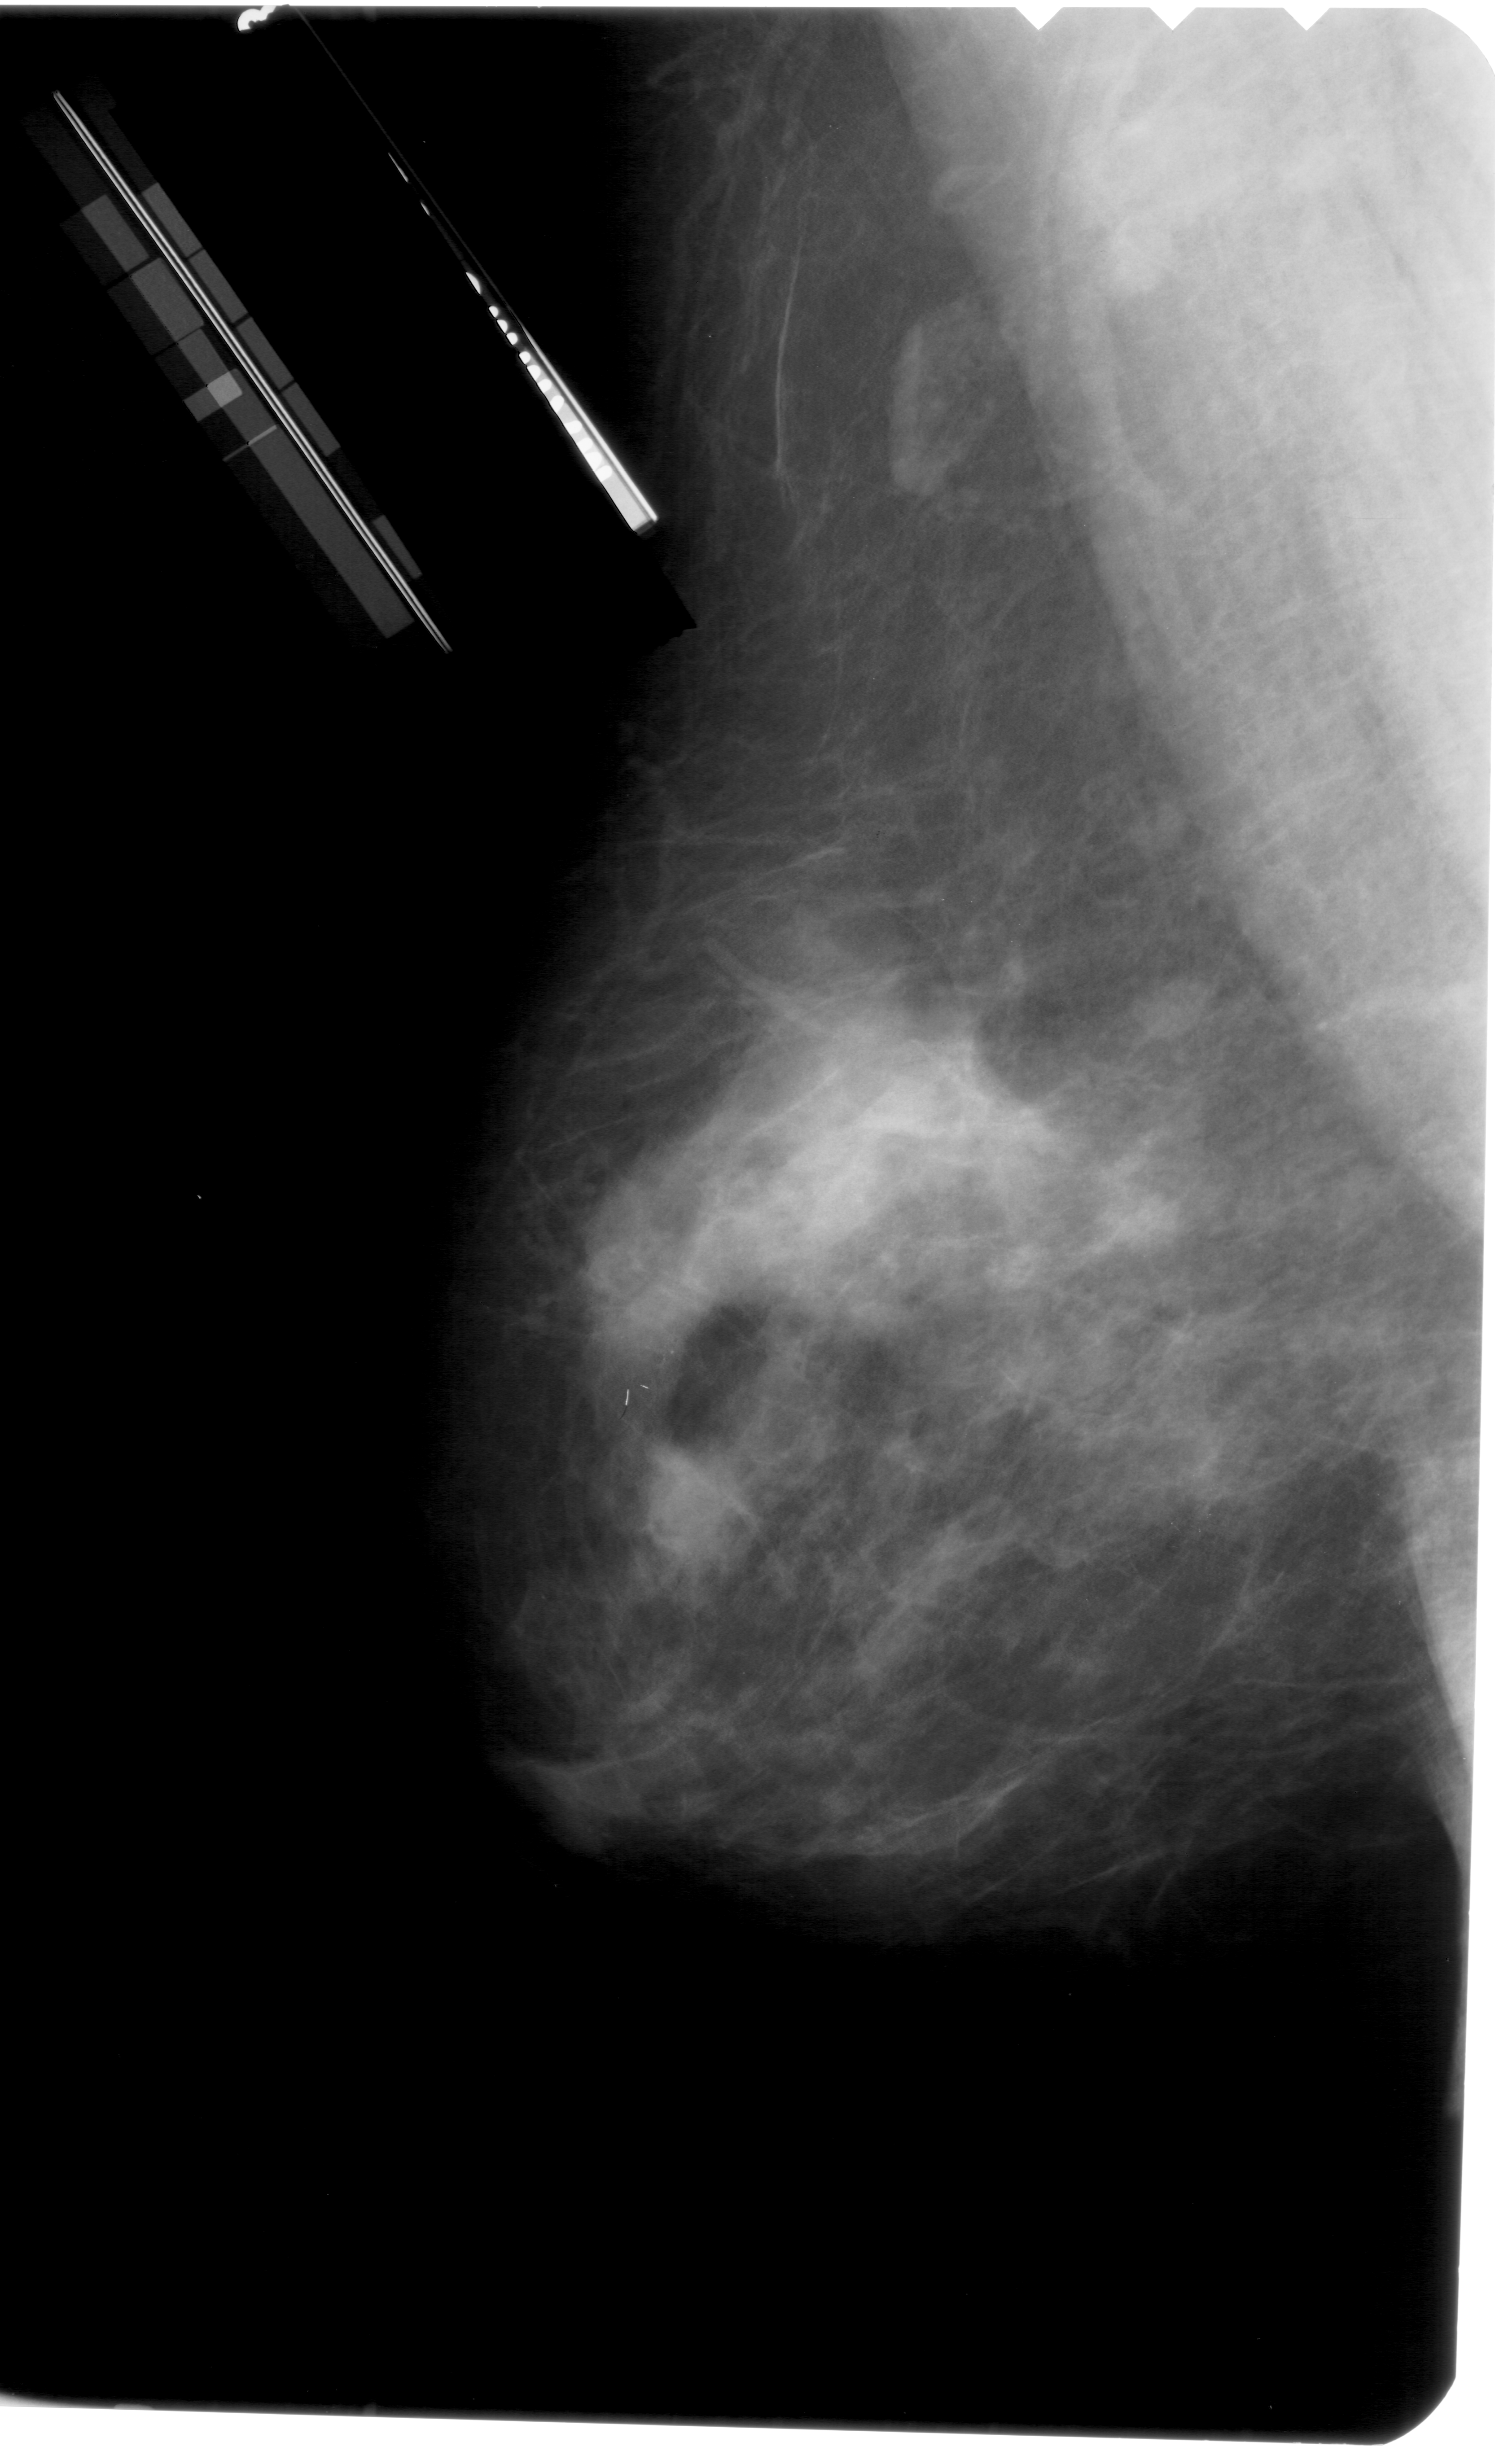
Digitized screen-film mammogram; left breast; mediolateral oblique (MLO) view; BI-RADS breast density category 4 (scale 1–4).
- Abnormality record for this image: calcifications, morphology pleomorphic, distribution clustered; BI-RADS assessment category 4; pathology (as recorded): benign.